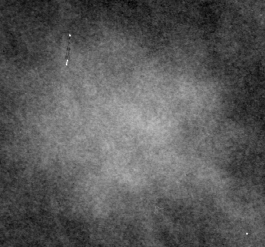
Cropped region of a digitized screen-film mammogram centred on a radiologist-marked abnormality, left breast, MLO view.
Mass, shape irregular, margins spiculated; BI-RADS assessment category 4; subtlety rating 4 on a 1 (subtle) to 5 (obvious) scale; pathology result (as recorded, not read from the image): malignant.